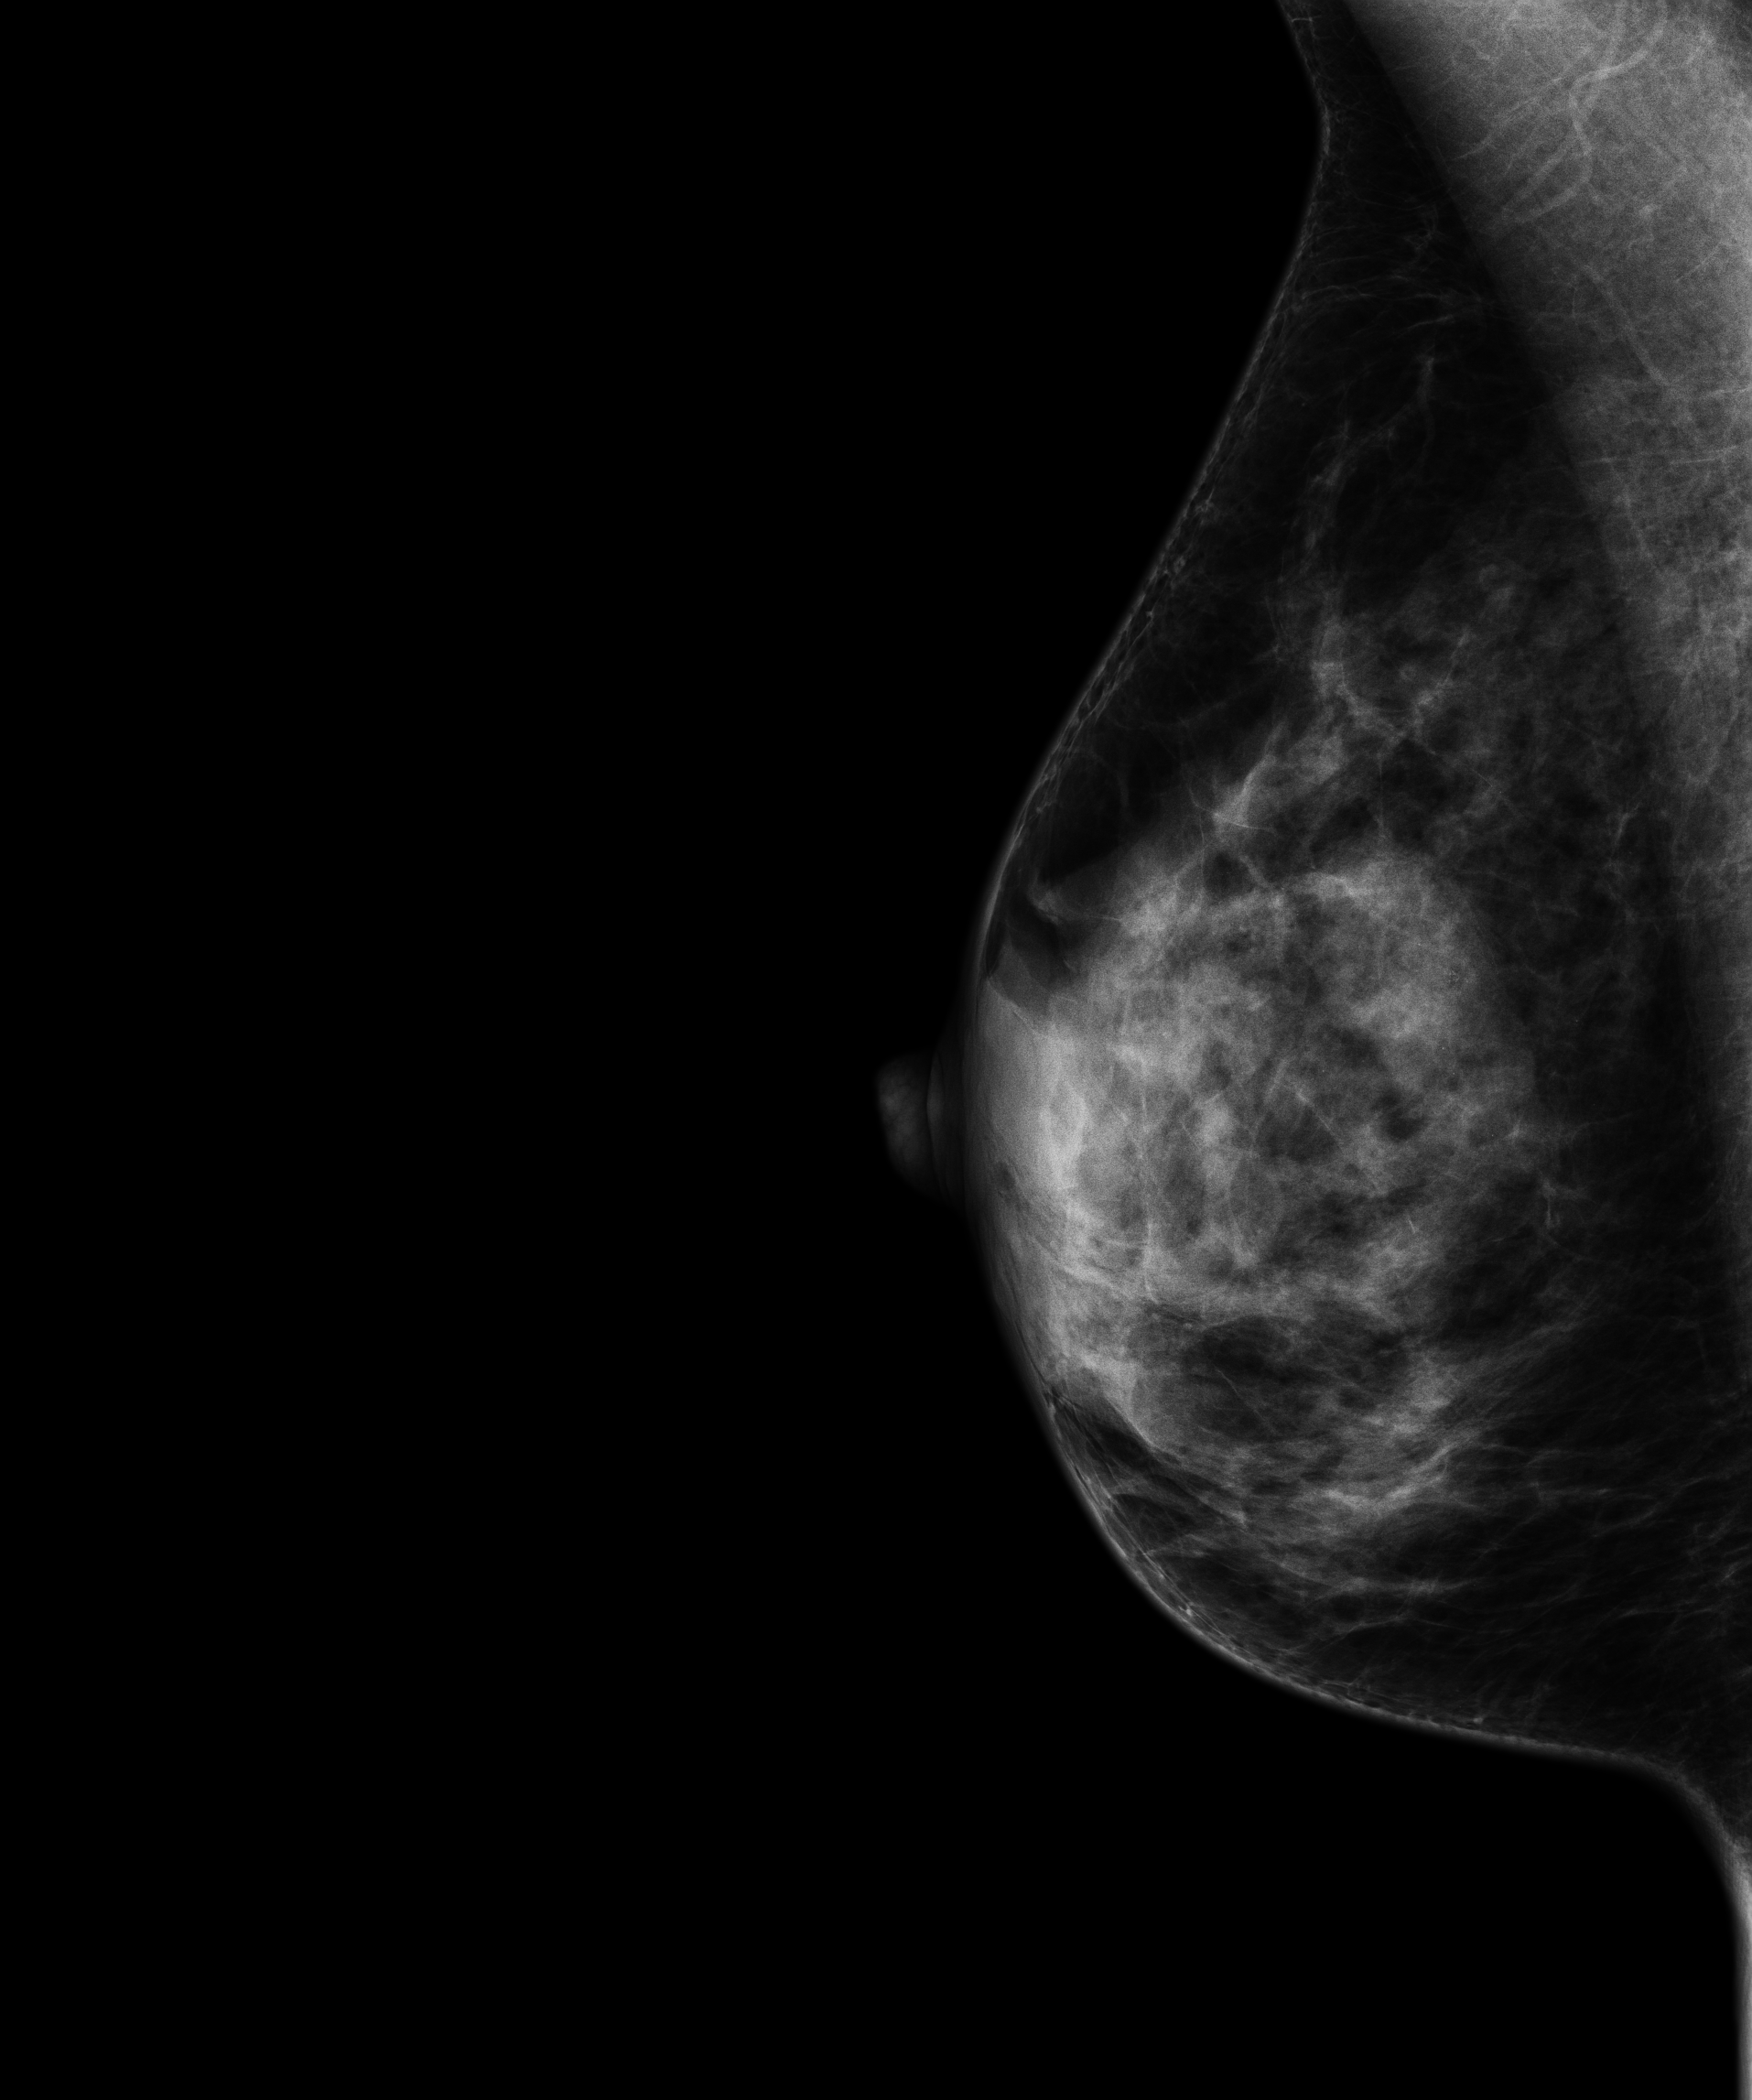
Full-field digital mammogram (FFDM); right breast; mediolateral oblique (MLO) view; screening examination; system: Senographe Essential ADS_56.21.3. Patient aged 56 years (female).
- BI-RADS breast density category at the screening exam (both breasts, scale 1–4): 4
- final BI-RADS assessment for this screening round (tomosynthesis exam, both breasts): category 1
- recall: no recall after this screen